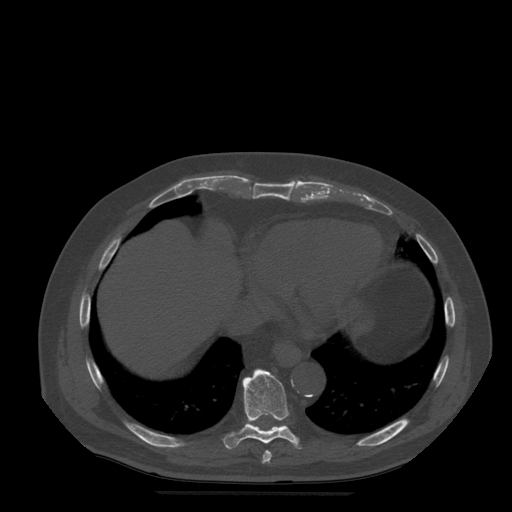
CT including the spine, one axial slice; position 290 of 522 along the scan axis; bone window (W 1800 / L 400 HU); 1.25 mm slice thickness; 512 × 512 image matrix, field of view 420 × 420 mm. Patient age 72 years. Case-level facts recorded for this patient, not image findings: primary cancer: prostate.
Outlined on this slice (semi-automatically segmented with operator editing):
- T8 vertebra: box from (x=262, y=451) to (x=272, y=464) px
- T9 vertebra: (x=223, y=369)–(x=301, y=449)